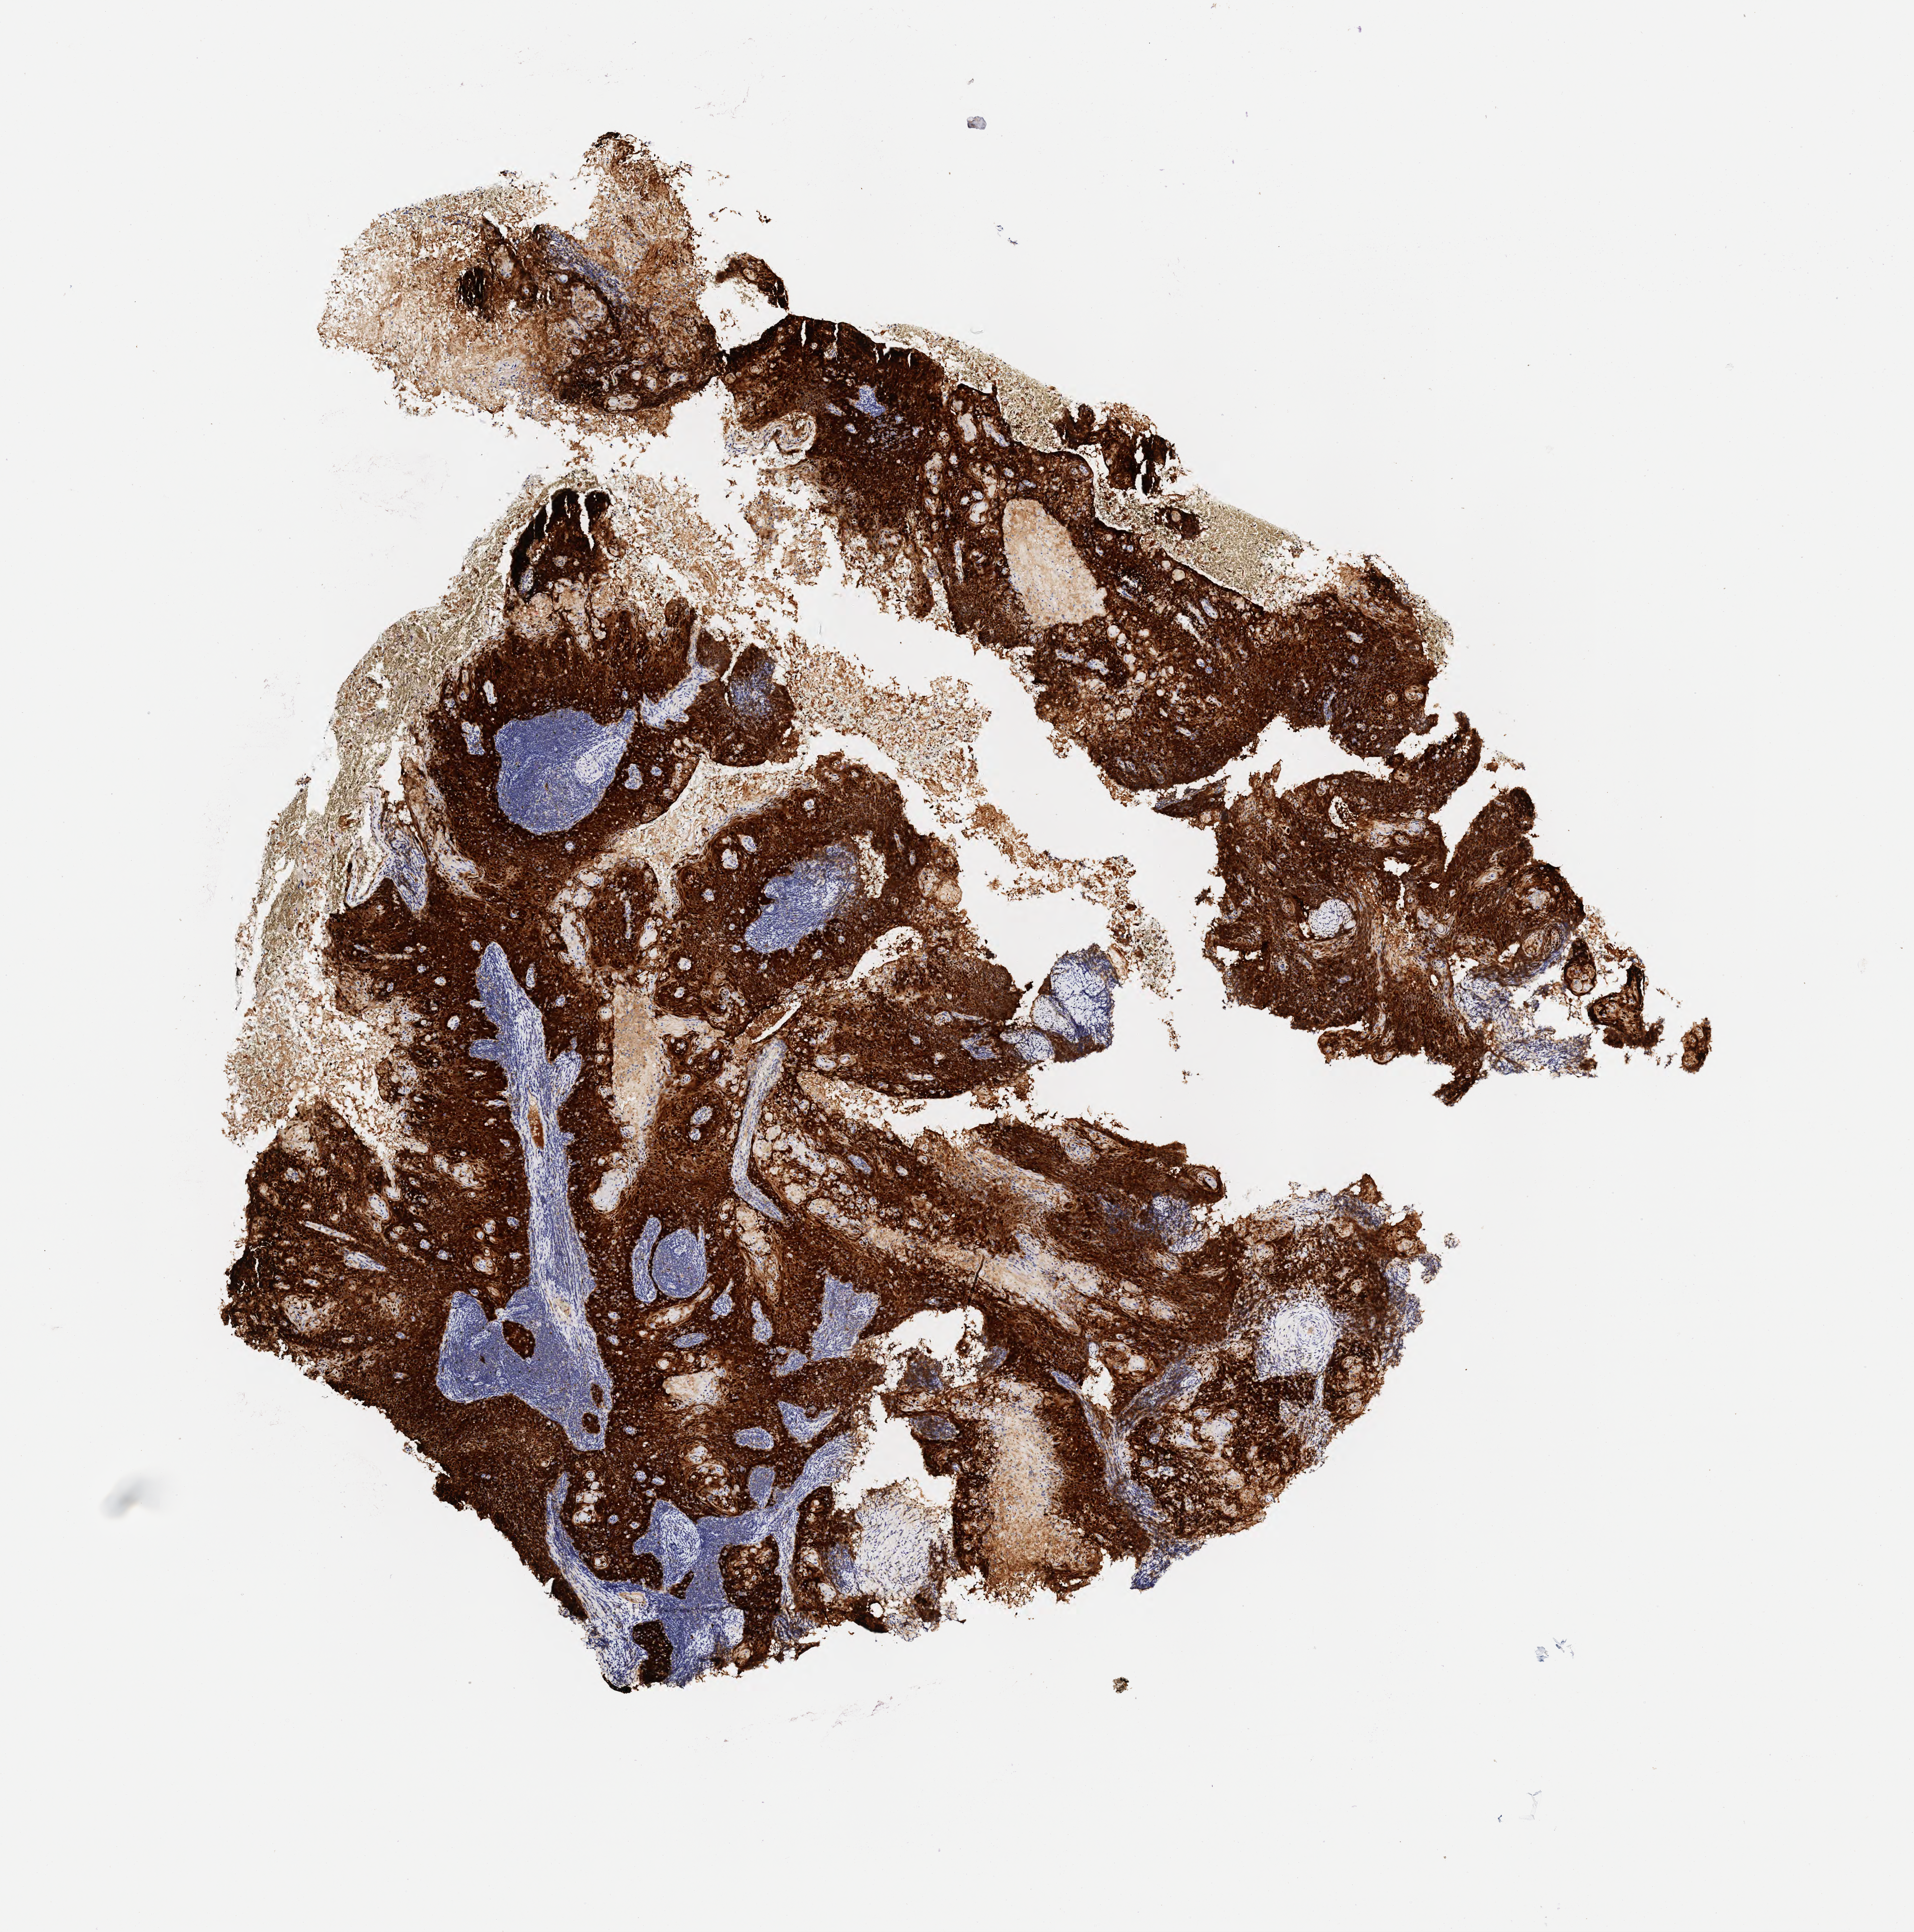
Whole-slide image, immunohistochemical stain for p16 (p16INK4a), whole scanned area (about 6.0 x 6.1 mm) shown as a low-resolution overview. Specimen: tumor tissue. Site: cervix. Patient female; 56 years old.
Diagnosis: Squamous cell carcinoma, keratinizing, NOS.